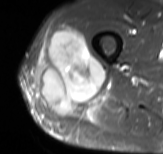
MRI of an extremity soft-tissue mass, one axial slice. Position 38 of 61 along the scan axis. STIR. MR volume resampled by the dataset authors to the PET/CT grid (not the native acquisition matrix). 3.27 mm slice thickness. 163 × 154 image matrix. Male patient. From the clinical record (not read from this slice): histological type: poorly differentiated synovial sarcoma; grade: high; site of the primary tumour: right buttock.
Annotated regions visible in this slice (expert contour drawn on MRI and transferred to this co-registered scan by the dataset authors):
- gross tumour volume including surrounding oedema: bounding box (x1, y1, x2, y2) in pixels: (39, 28, 106, 113)
- gross tumour volume (mass): (41, 28, 106, 113)